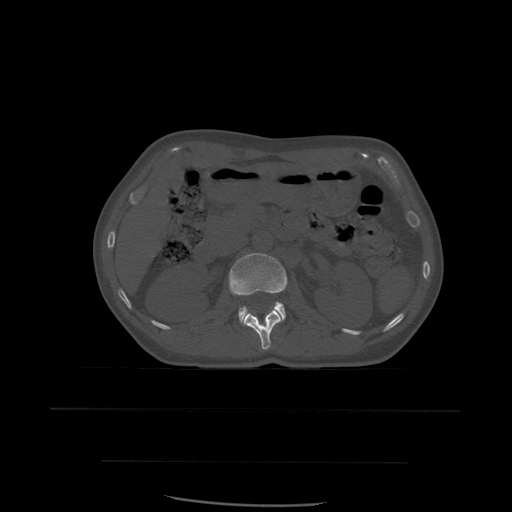
CT including the spine, one axial slice. Slice 237 of 574 in the series (ordered by position). Bone window (W 1800 / L 400 HU). 512 × 512 image matrix, field of view 392 × 392 mm. Patient age 48 years. From the clinical record (not read from this slice): primary cancer: lung.
Outlined on this slice (semi-automatically segmented with operator editing):
- L1 vertebra: box from (x=243, y=310) to (x=283, y=351) px
- L2 vertebra: (x=229, y=253)–(x=288, y=323)